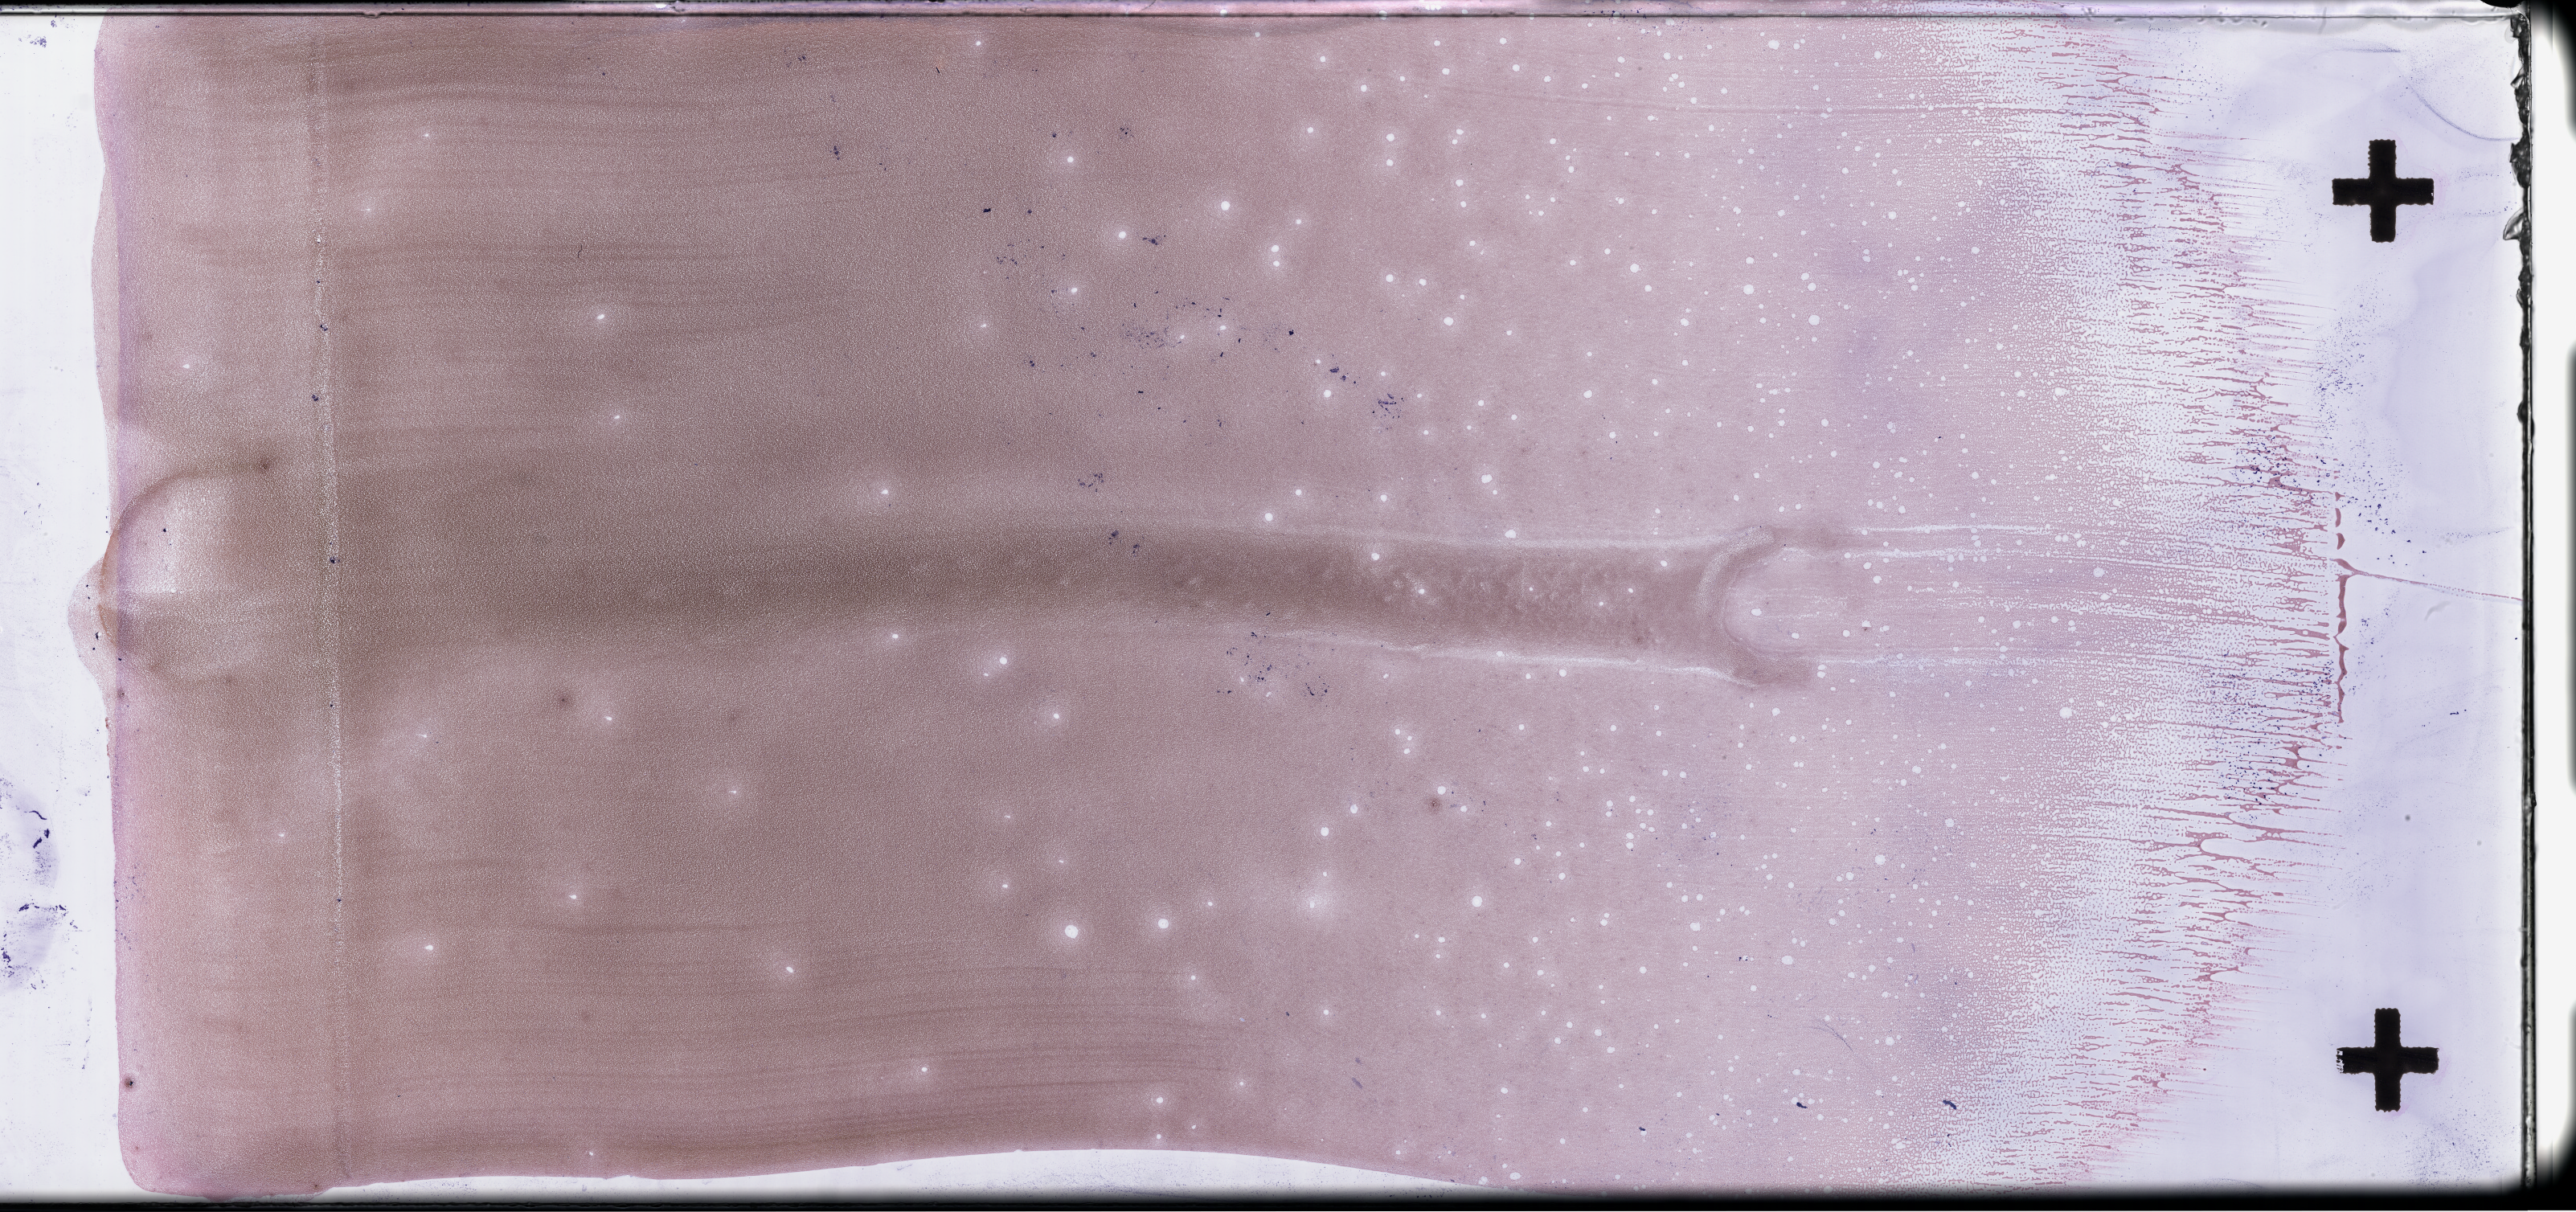
Whole-slide image of a whole blood smear, Wright-Giemsa stain — shown as a low-resolution overview of the whole scanned area (about 51.8 x 24.4 mm). Smear from an EDTA sample. Patient sex: female.
Patient diagnosis: Plasma Cell Myeloma.